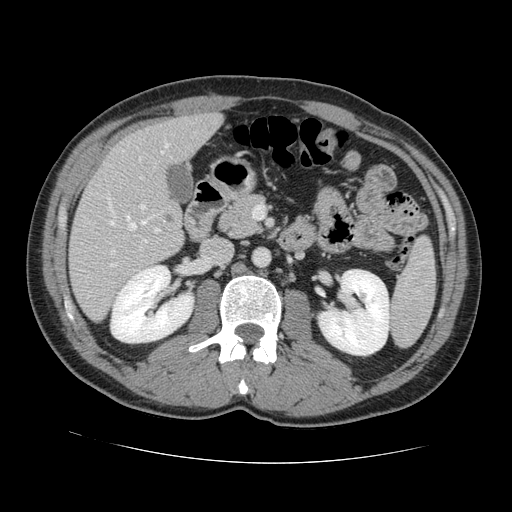
Contrast-enhanced abdominal CT, one axial slice; slice 61 of 131 in the series (ordered by position); intravenous contrast given; soft-tissue window (W 400 / L 40 HU); 512 × 512 image matrix. Male patient, age 40 years. From the clinical record (not read from this slice): diagnosis: colorectal cancer liver metastases, imaged before liver resection; multiple liver metastases: yes; largest metastasis: 2.9 cm; chemotherapy before resection: yes.
Outlined on this slice (manually delineated by an expert):
- hepatic veins: box from (x=108, y=141) to (x=170, y=253) px
- liver: (x=70, y=114)–(x=220, y=320)
- planned liver remnant (the part of the liver to remain after resection): (x=111, y=114)–(x=220, y=178)
- portal vein (with intrahepatic branches): (x=110, y=158)–(x=160, y=267)
- liver metastasis: (x=164, y=216)–(x=175, y=225)